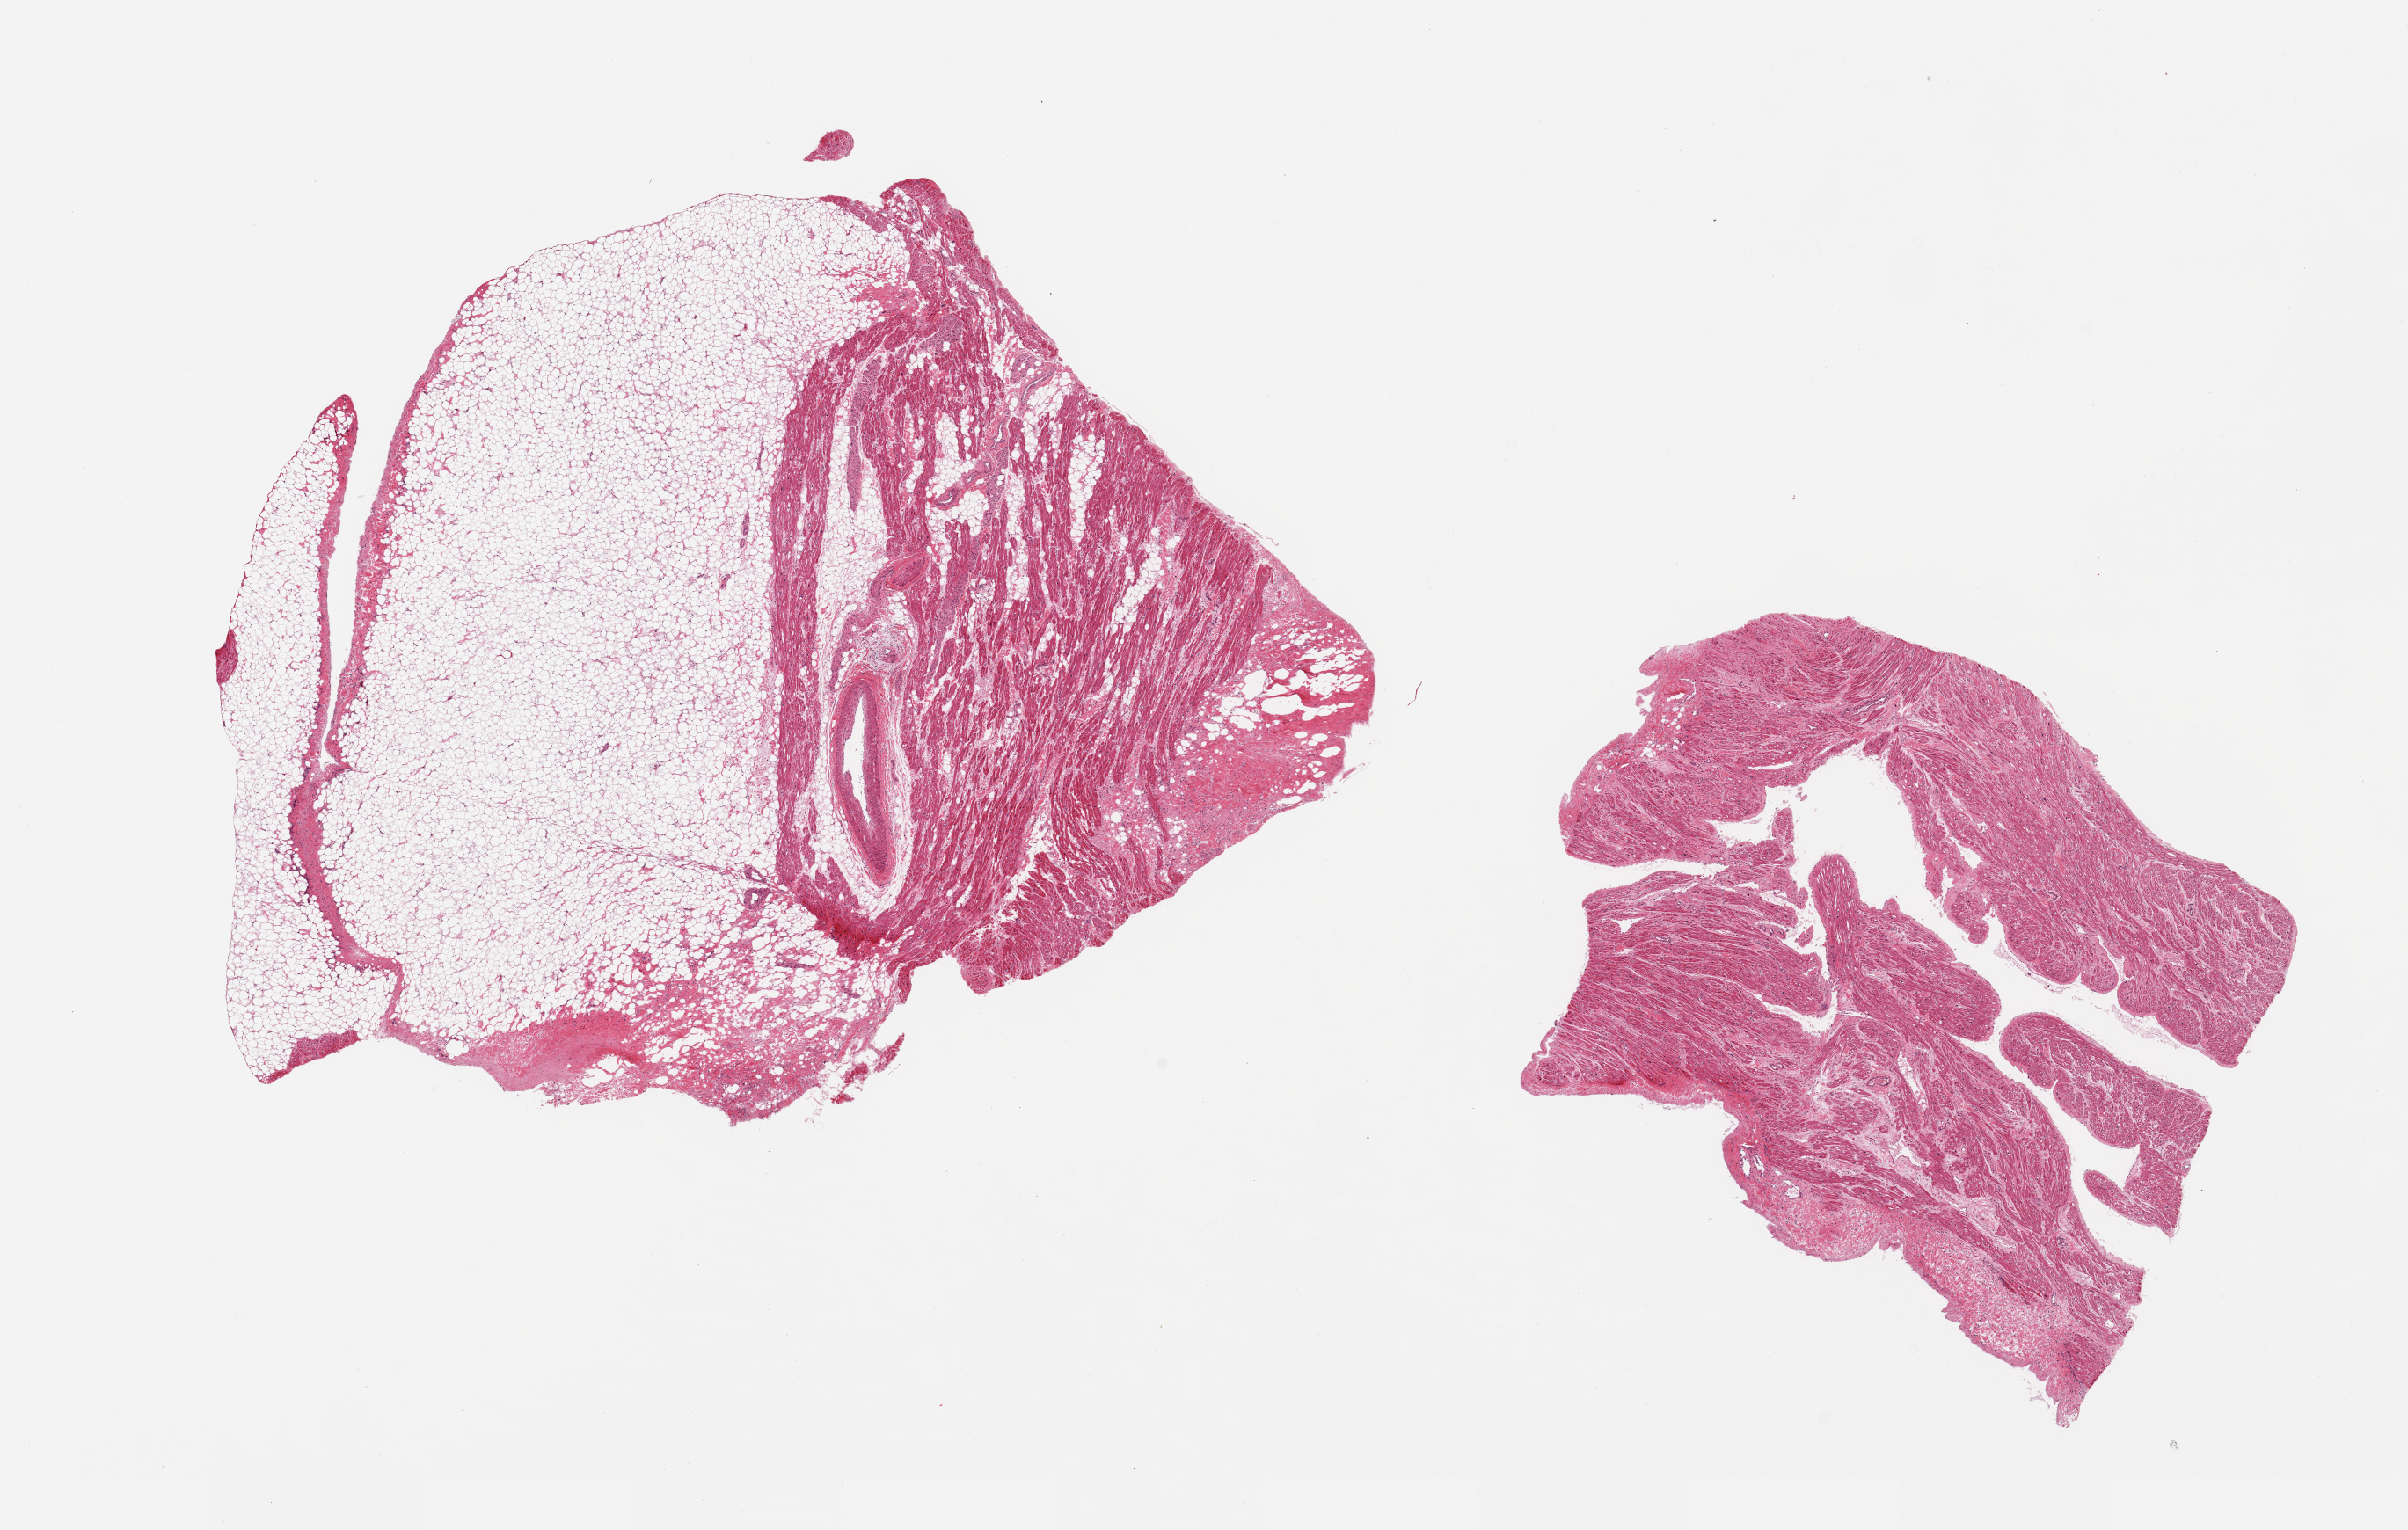
Whole-slide image, H&E stain — a low-resolution overview of the entire scanned area, about 21.7 x 13.8 mm. PAXgene-fixed paraffin-embedded (PFPE) section. Sampled site (target tissue): auricular appendage. Donor tissue sample. Donor: male.
• review note (as recorded): 2 pieces; one contains over 60% fat and fibrous tissue